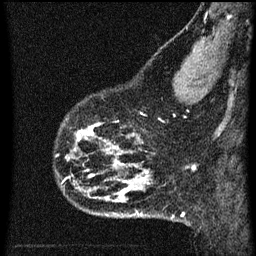
Breast MRI (dynamic contrast-enhanced), one sagittal slice. Slice 14 of 60 in the series (ordered by position). Dynamic contrast-enhanced series, image 2 of 3 at this slice position (ordered by acquisition). 1.5 T. TE 4.2 ms, TR 8 ms. 2 mm slice thickness. 256 × 256 image matrix. Female patient, age 43 years.
Outlined on this slice (semi-automatically segmented with operator editing):
- analysis volume of interest (the breast-tissue region the enhancement analysis was run in; not a lesion): bounding box (x1, y1, x2, y2) in pixels: (55, 104, 104, 153)
- tumour enhancement mask (voxels above the 70 % enhancement threshold inside the analysis volume of interest): (75, 122, 101, 141)